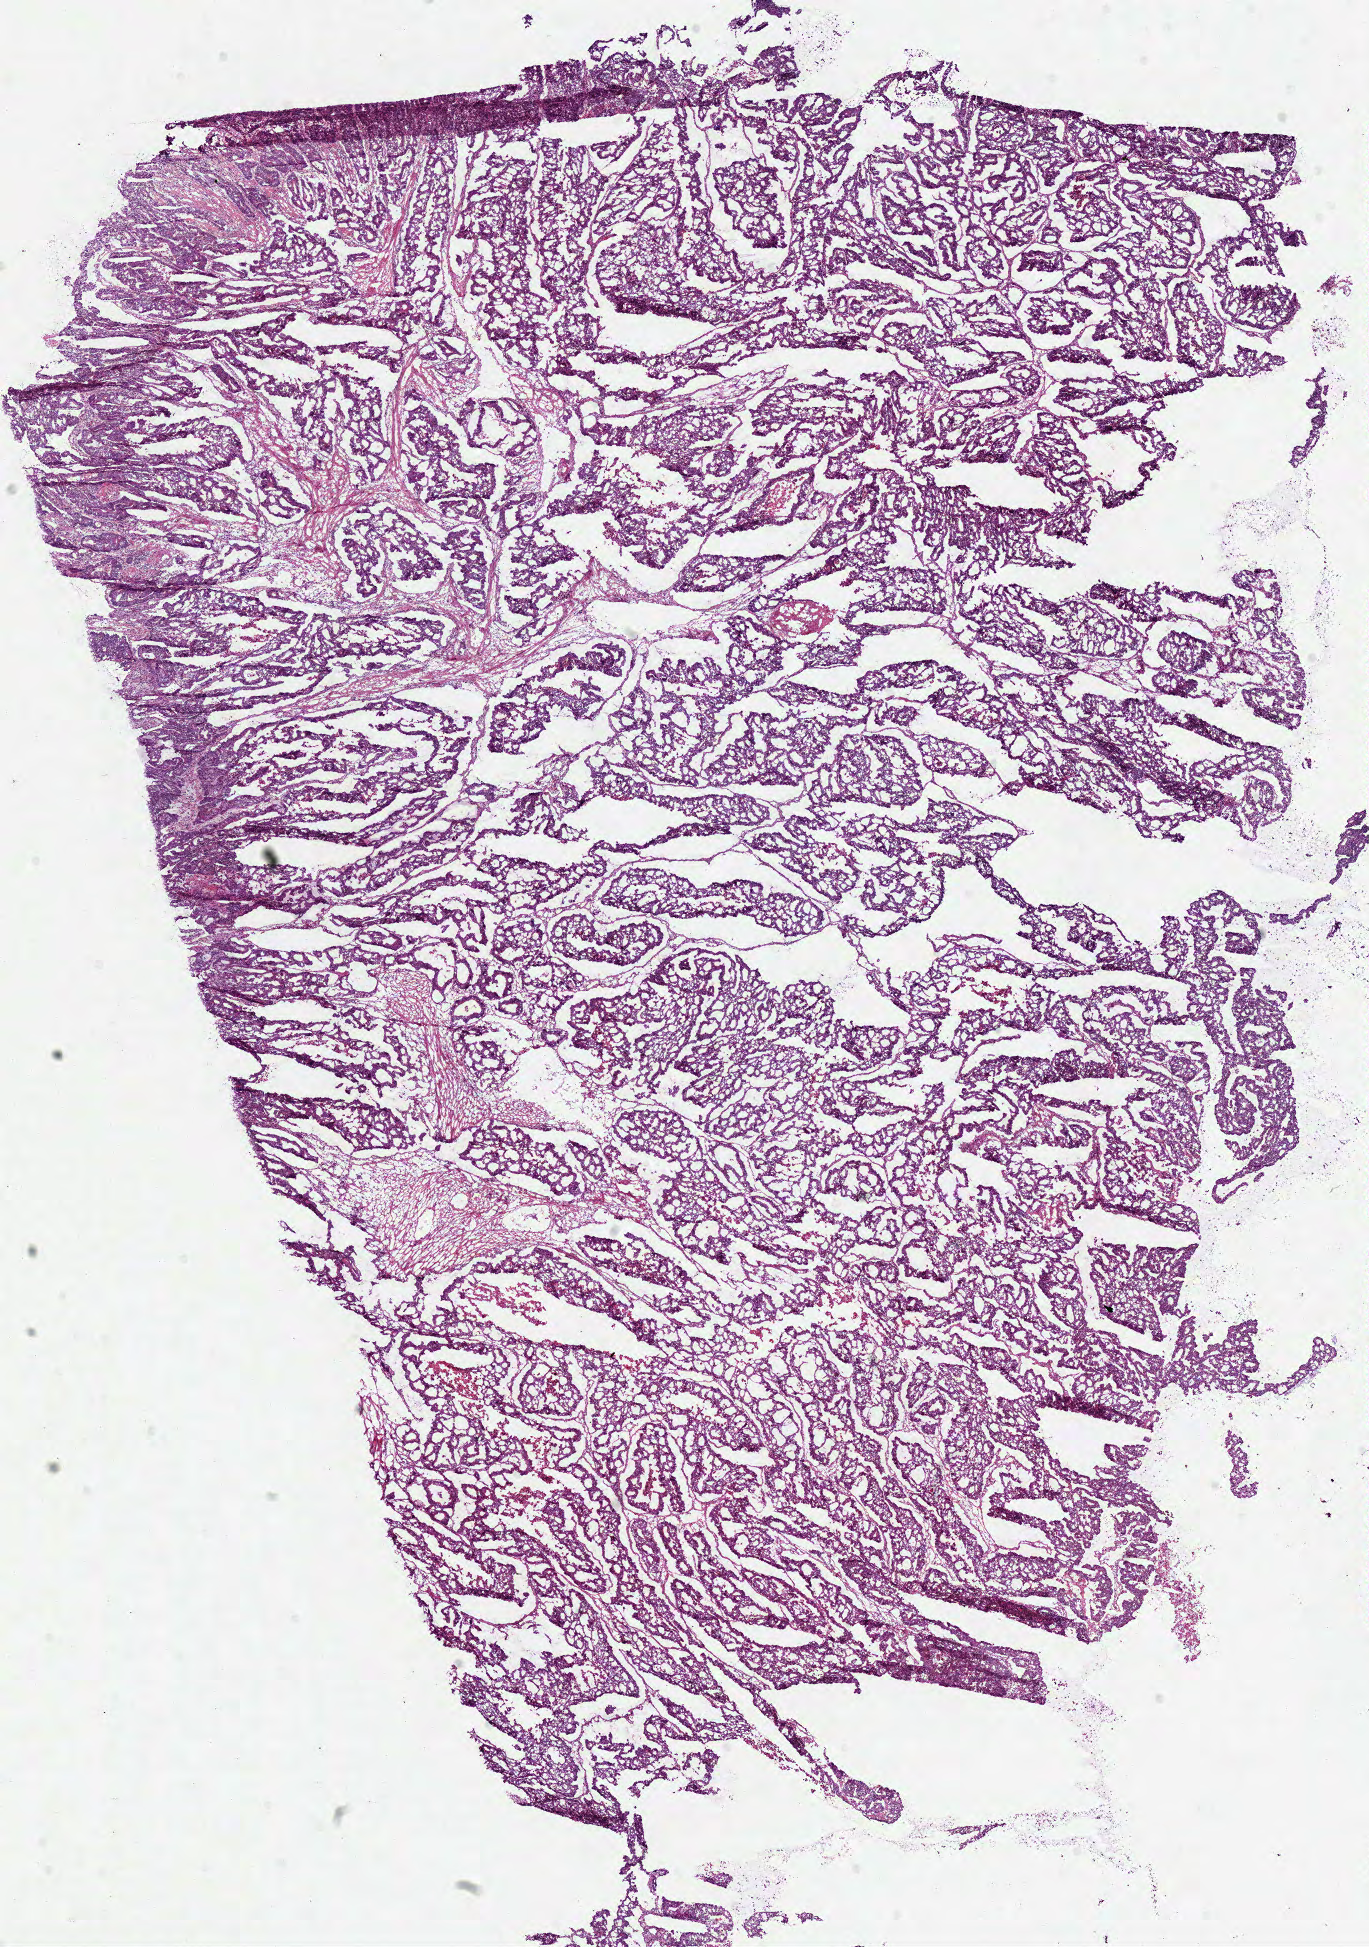
Whole-slide histology image, Hematoxylin and eosin (H&E) stained, whole scanned area (about 10.8 x 15.3 mm) shown as a low-resolution overview. Frozen section from the top of the tissue portion. Primary tumour sample from the colon. Patient: female, age at initial diagnosis 55 years. Pathologist review of this section (percent, as recorded): tumour cells 87%, tumour nuclei 80%, normal cells 0%, stromal cells 10%, necrosis 3%.
Lymph nodes positive (case pathology): 2 of 12 examined. Pathologic diagnosis: Adenocarcinoma, NOS. AJCC pathologic stage: IIIA (6th edition).